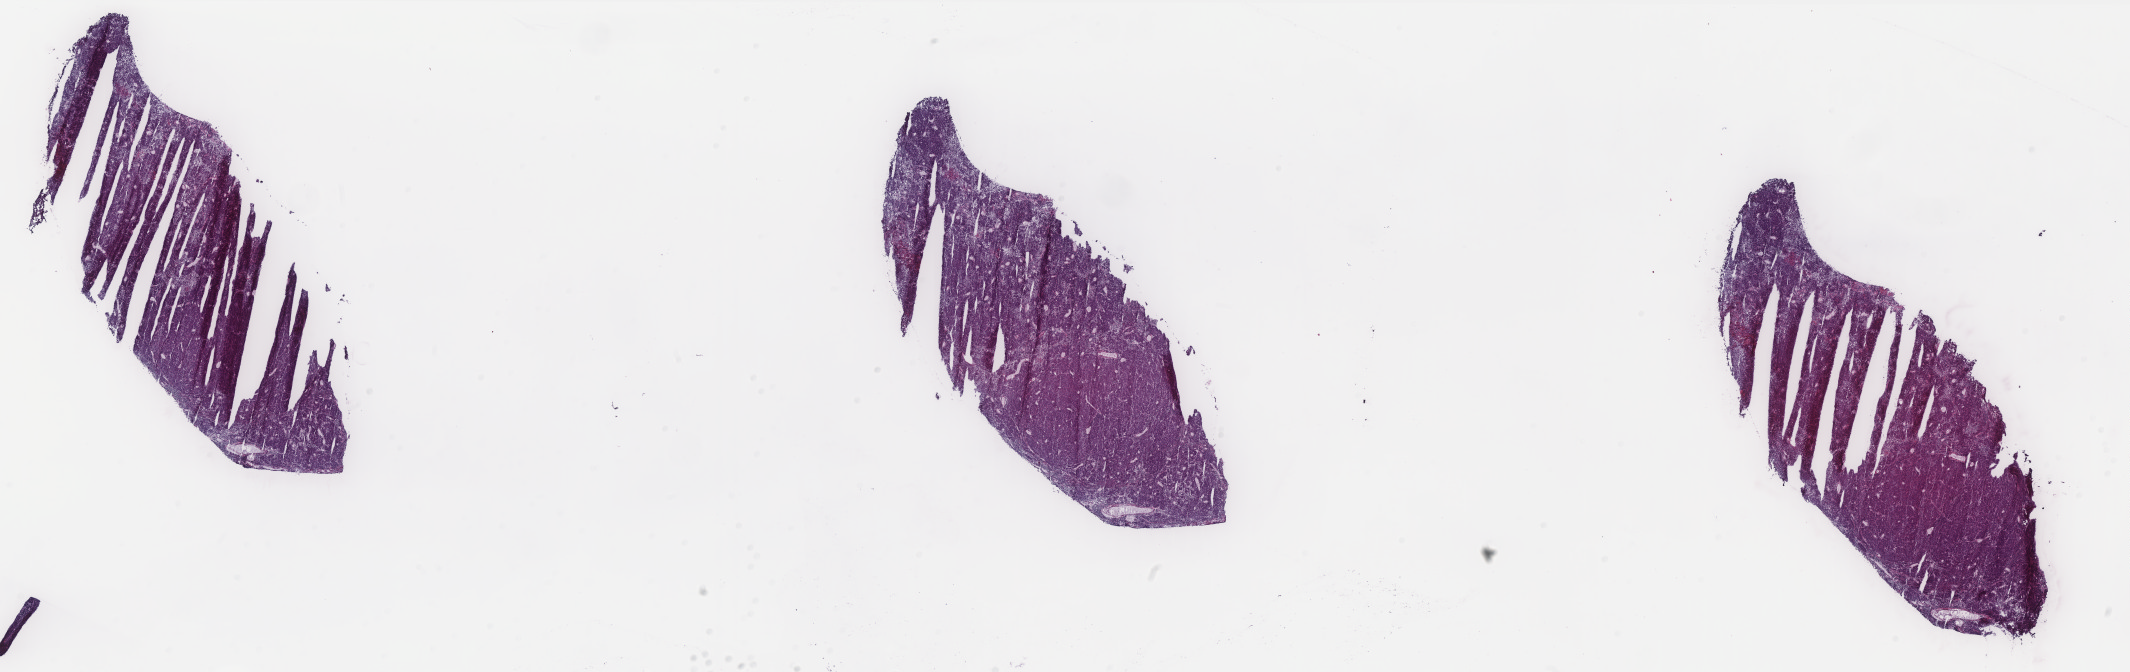
Whole-slide histology image, H&E-stained — whole scanned area (about 34.2 x 10.8 mm) shown as a low-resolution overview, frozen section from the top of the tissue portion, primary tumour sample from the uterus. Patient: female, age at initial diagnosis 62 years. Histologic grade: G3 (poorly differentiated). Slide review estimates, as recorded: tumour cells 100%, tumour nuclei 85%, normal cells 0%, stromal cells 0%, necrosis 0%. Inflammatory infiltration, as recorded: lymphocyte infiltration 0%, monocyte infiltration 0%, neutrophil infiltration 0%.
* FIGO stage: IB
* diagnosis: Endometrioid adenocarcinoma, NOS (endometrium)